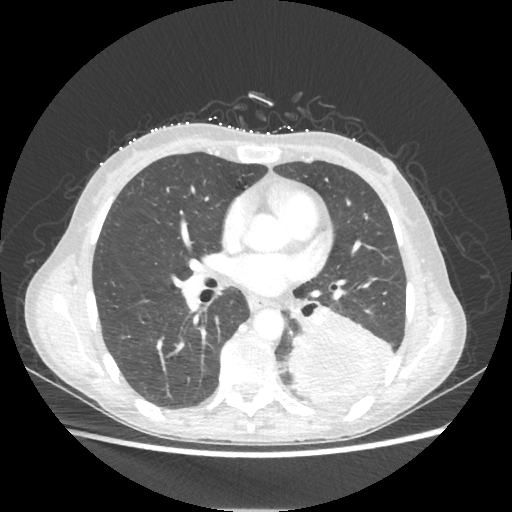
Chest CT, one axial slice; position 110 of 221 along the scan axis; 80 kVp; lung window (W 1500 / L -600 HU); 1.25 mm slice thickness; 512 × 512 image matrix, field of view 360 × 360 mm. Patient: female, 53 years. From the clinical record (not read from this slice): clinical TNM (as recorded): T3 N0 M0.
Annotated regions visible in this slice (bounding box drawn by a radiologist):
- lung tumour (recorded histology: adenocarcinoma): bounding box [x1, y1, x2, y2] px = [287, 308, 395, 405]